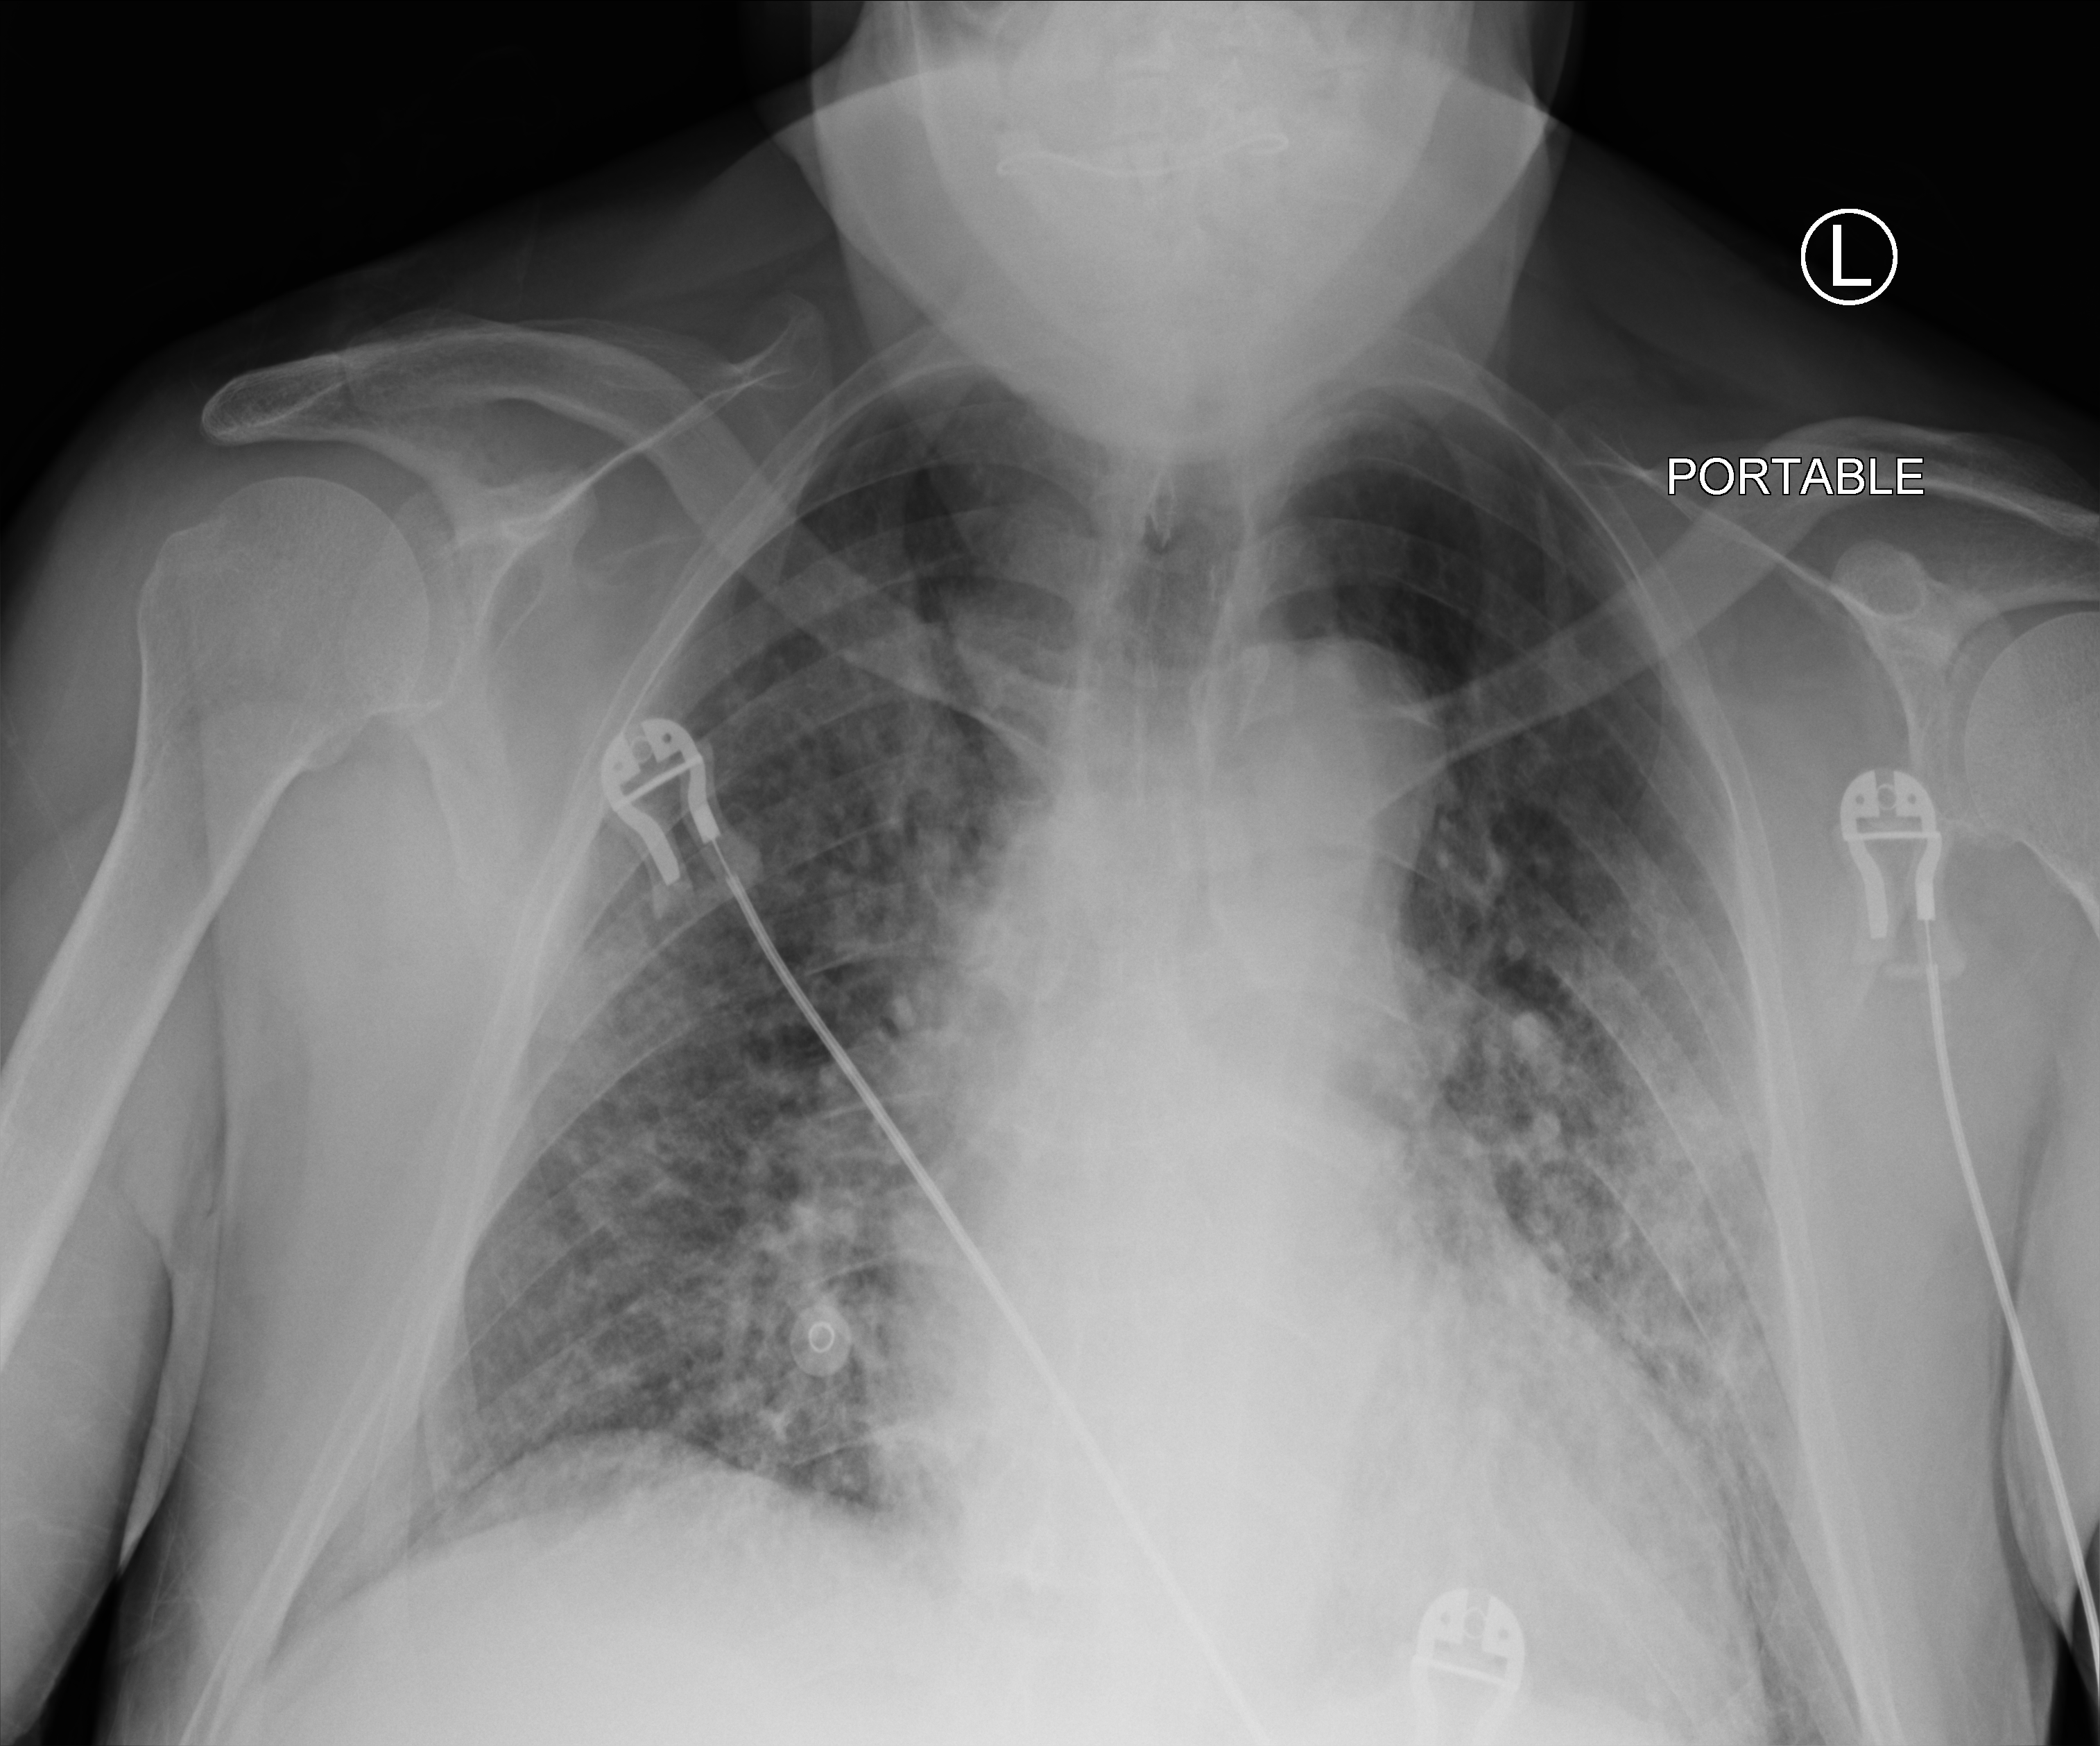
Chest X-ray (portable). Male patient hospitalised with COVID-19, age 60–74 years.
From the hospital-stay record, not from the radiograph (when in the stay this image was taken is not recorded): admitted to intensive care during this hospital stay: no.